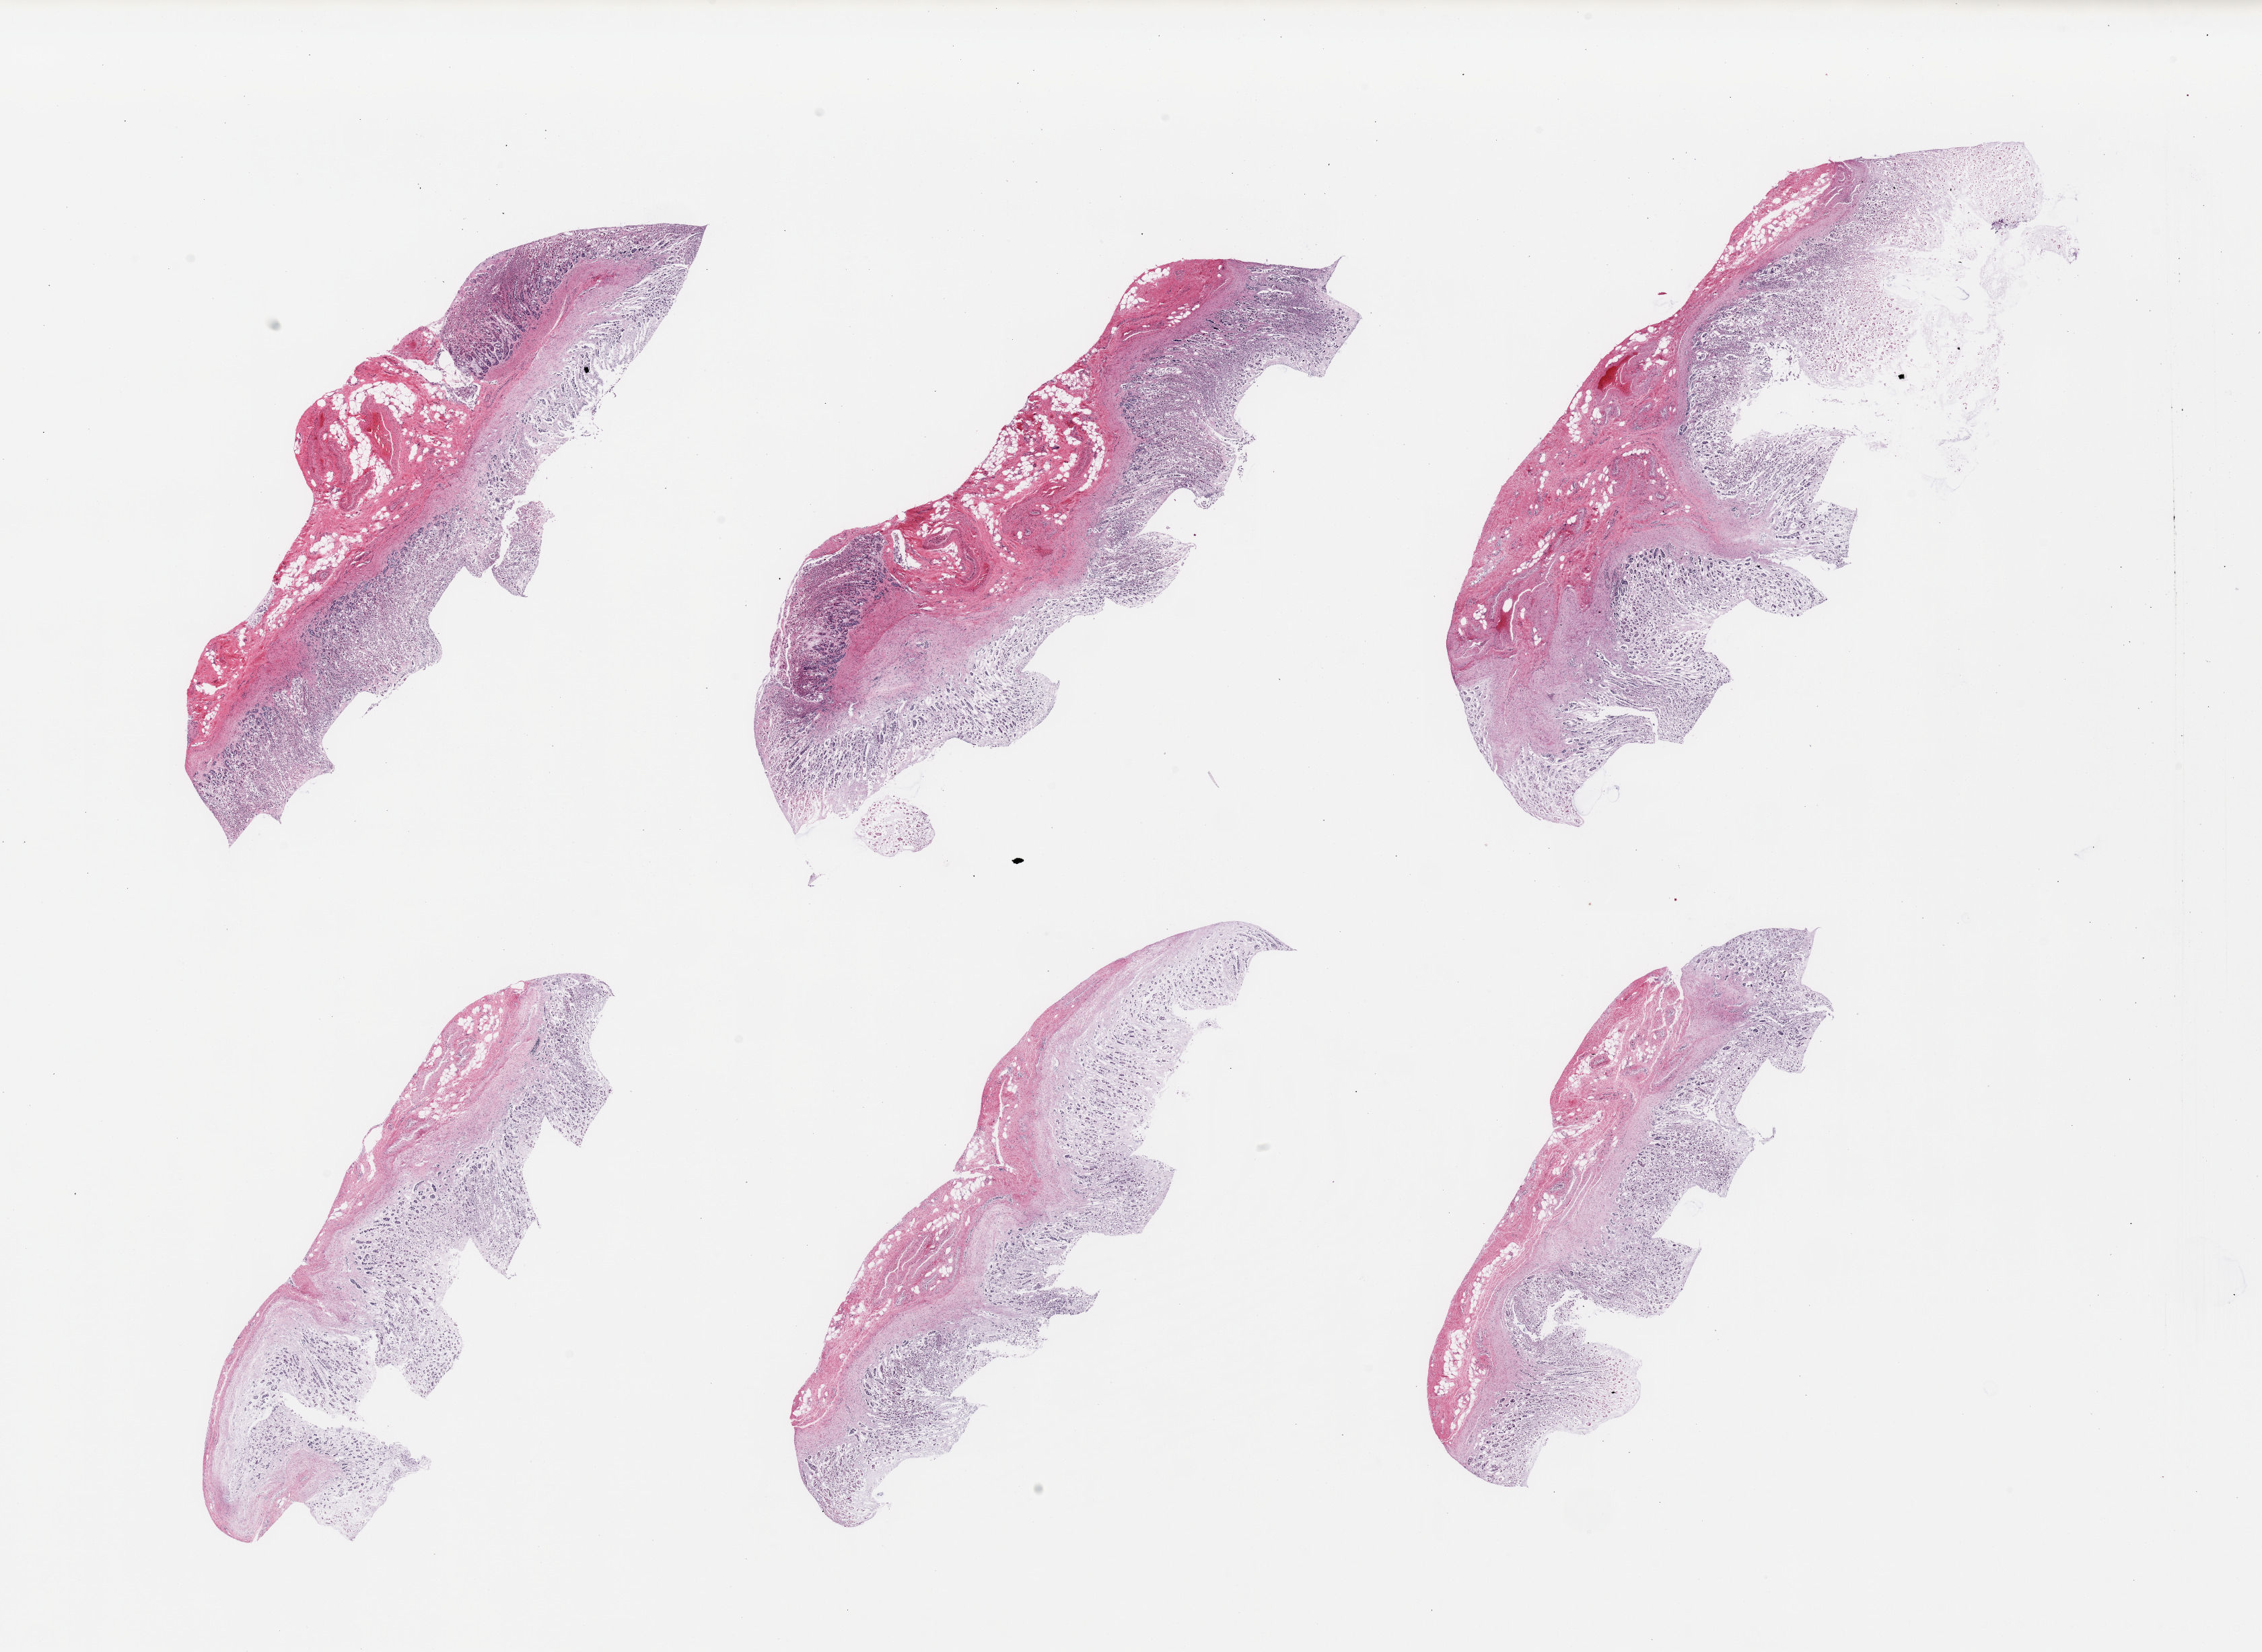
Whole-slide image, hematoxylin and eosin (H&E) stain, brightfield, low-resolution overview of the scanned area, about 26.6 x 19.4 mm (from a 20x scan), PAXgene-fixed, paraffin-embedded tissue, sampled site (target tissue): stomach, tissue donor sample. Male donor.
* review note (as recorded): 6 pieces; completely autolyzed mucosa; no muscularis